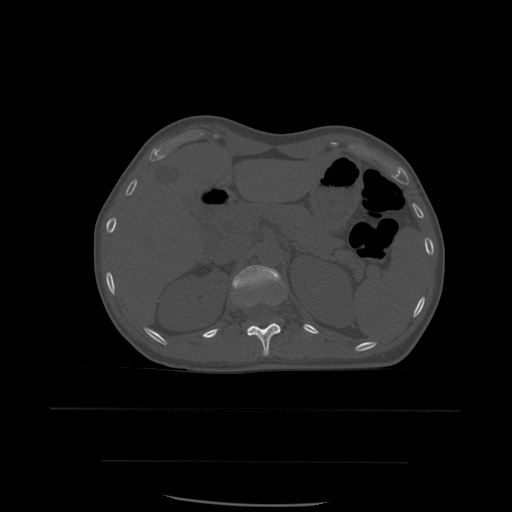
CT including the spine, one axial slice; position 265 of 574 along the scan axis; bone window (W 1800 / L 400 HU); 1.25 mm slice thickness; 512 × 512 image matrix. Patient age 48 years. From the clinical record (not read from this slice): primary cancer: lung.
Outlined on this slice (semi-automatic segmentation, software-assisted and operator-edited):
- L1 vertebra: bounding box (x1, y1, x2, y2) in pixels: (232, 266, 282, 294)
- T12 vertebra: (247, 303, 281, 357)